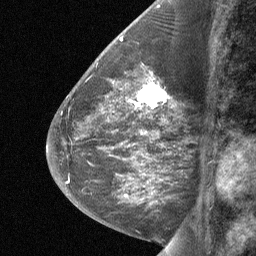
Breast MRI (dynamic contrast-enhanced), one sagittal slice. Slice 28 of 64 in the series (ordered by position). Dynamic contrast-enhanced study with each time point stored as its own series, time point 2 of 3 at this slice position (early post-contrast, ordered by acquisition time). 1.5 T. TE 4.8 ms, TR 27 ms. 256 × 256 image matrix, field of view 180 × 180 mm. Female patient, age 59 years. From the clinical record (not read from this slice): setting: breast cancer imaged before/during neoadjuvant chemotherapy; receptor status: triple-negative.
Annotated regions visible in this slice (semi-automatic segmentation, software-assisted and operator-edited):
- analysis volume of interest (the breast-tissue region the enhancement analysis was run in; not a lesion): bounding box (x1, y1, x2, y2) in pixels: (126, 75, 173, 114)
- tumour enhancement mask (voxels above the 90 % enhancement threshold inside the analysis volume of interest): (129, 78, 168, 110)